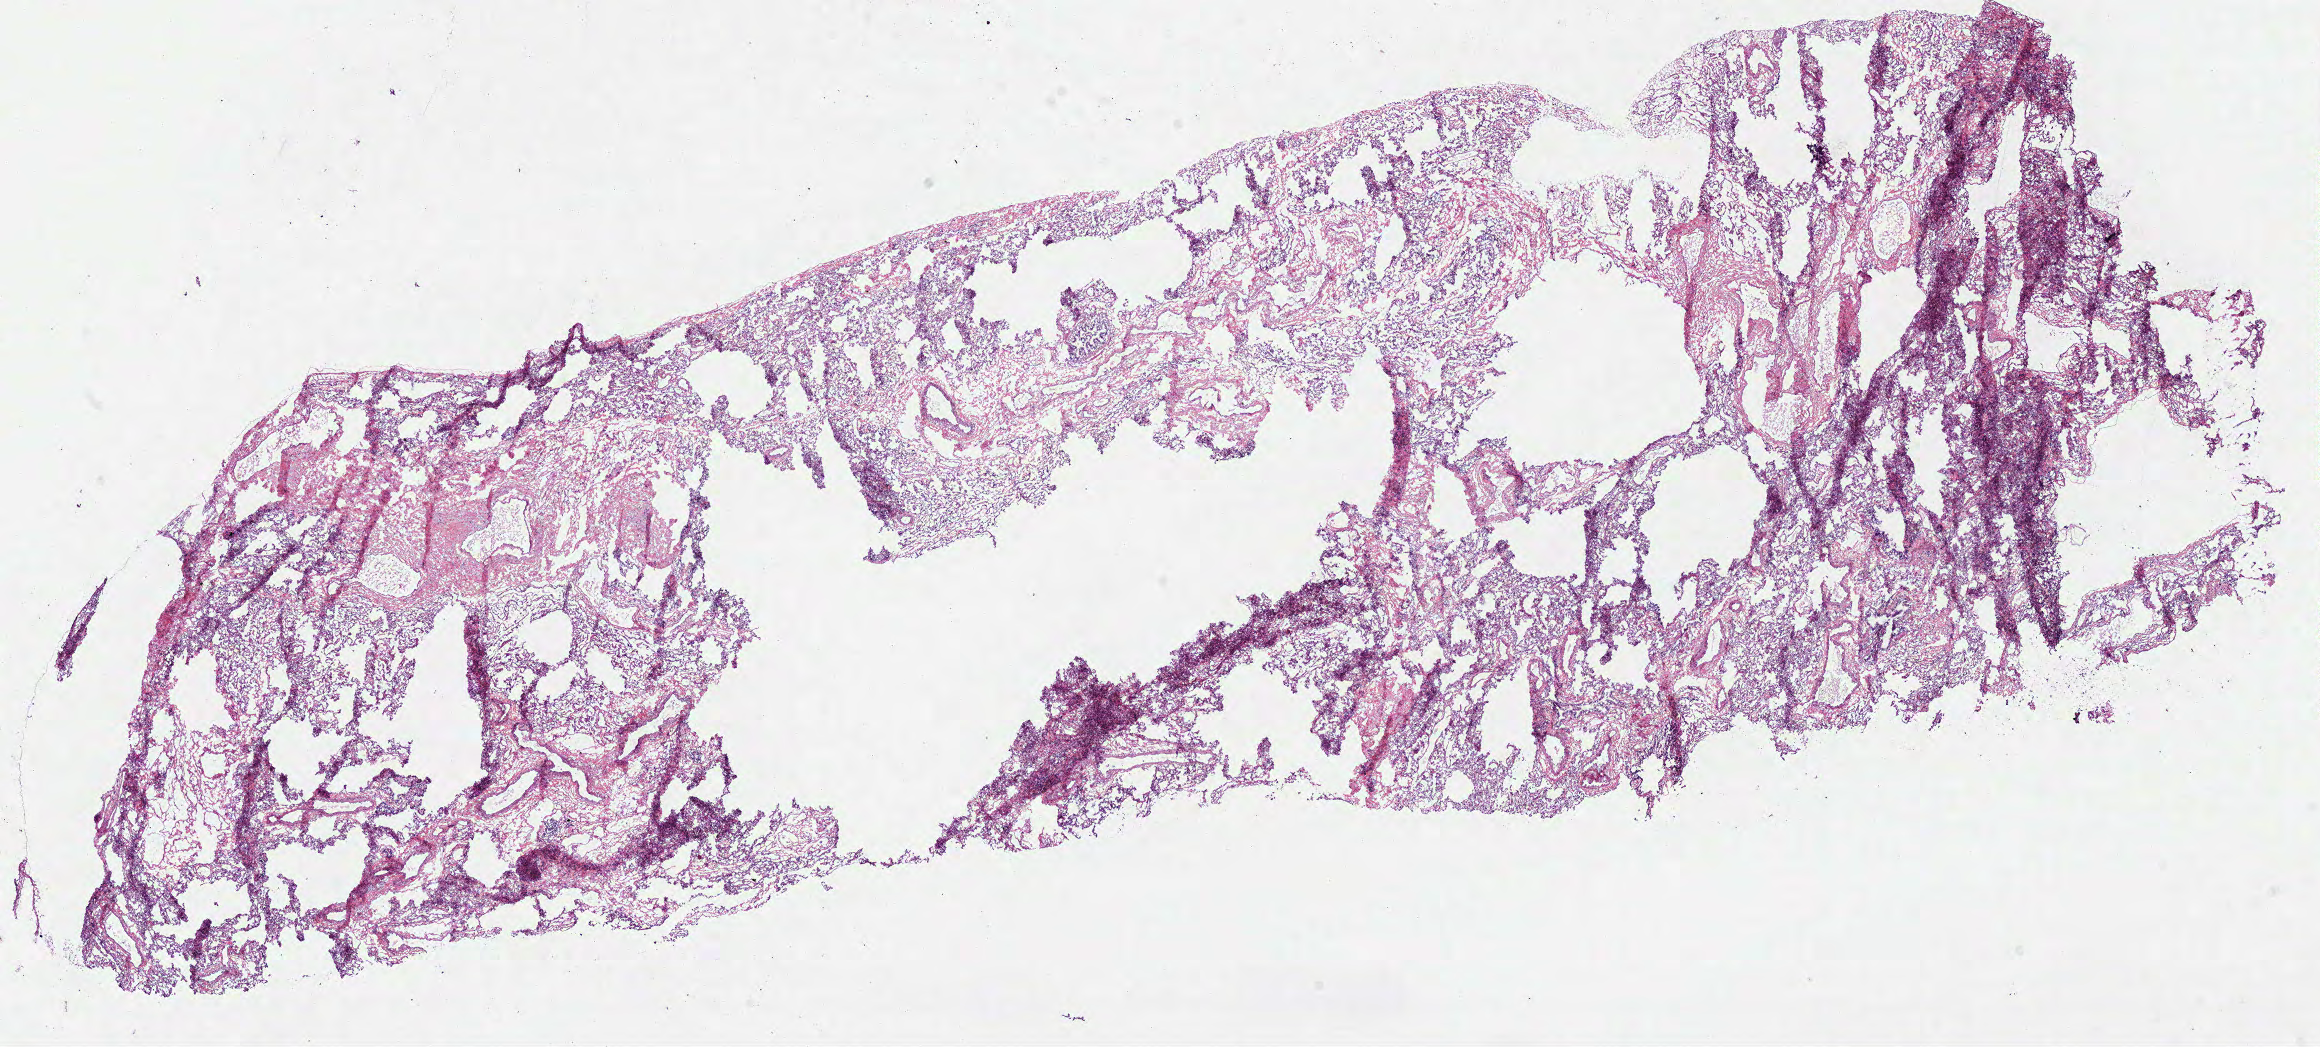
H&E whole-slide image — whole scanned area (about 18.3 x 8.3 mm) shown as a low-resolution overview; frozen section from the top of the tissue portion; lung, solid tissue normal (non-tumour tissue) sample. Male patient; age at initial diagnosis 82 years.
This section: solid tissue normal sample (biorepository sample class). Patient diagnosis: Papillary adenocarcinoma, NOS (upper lobe, lung).